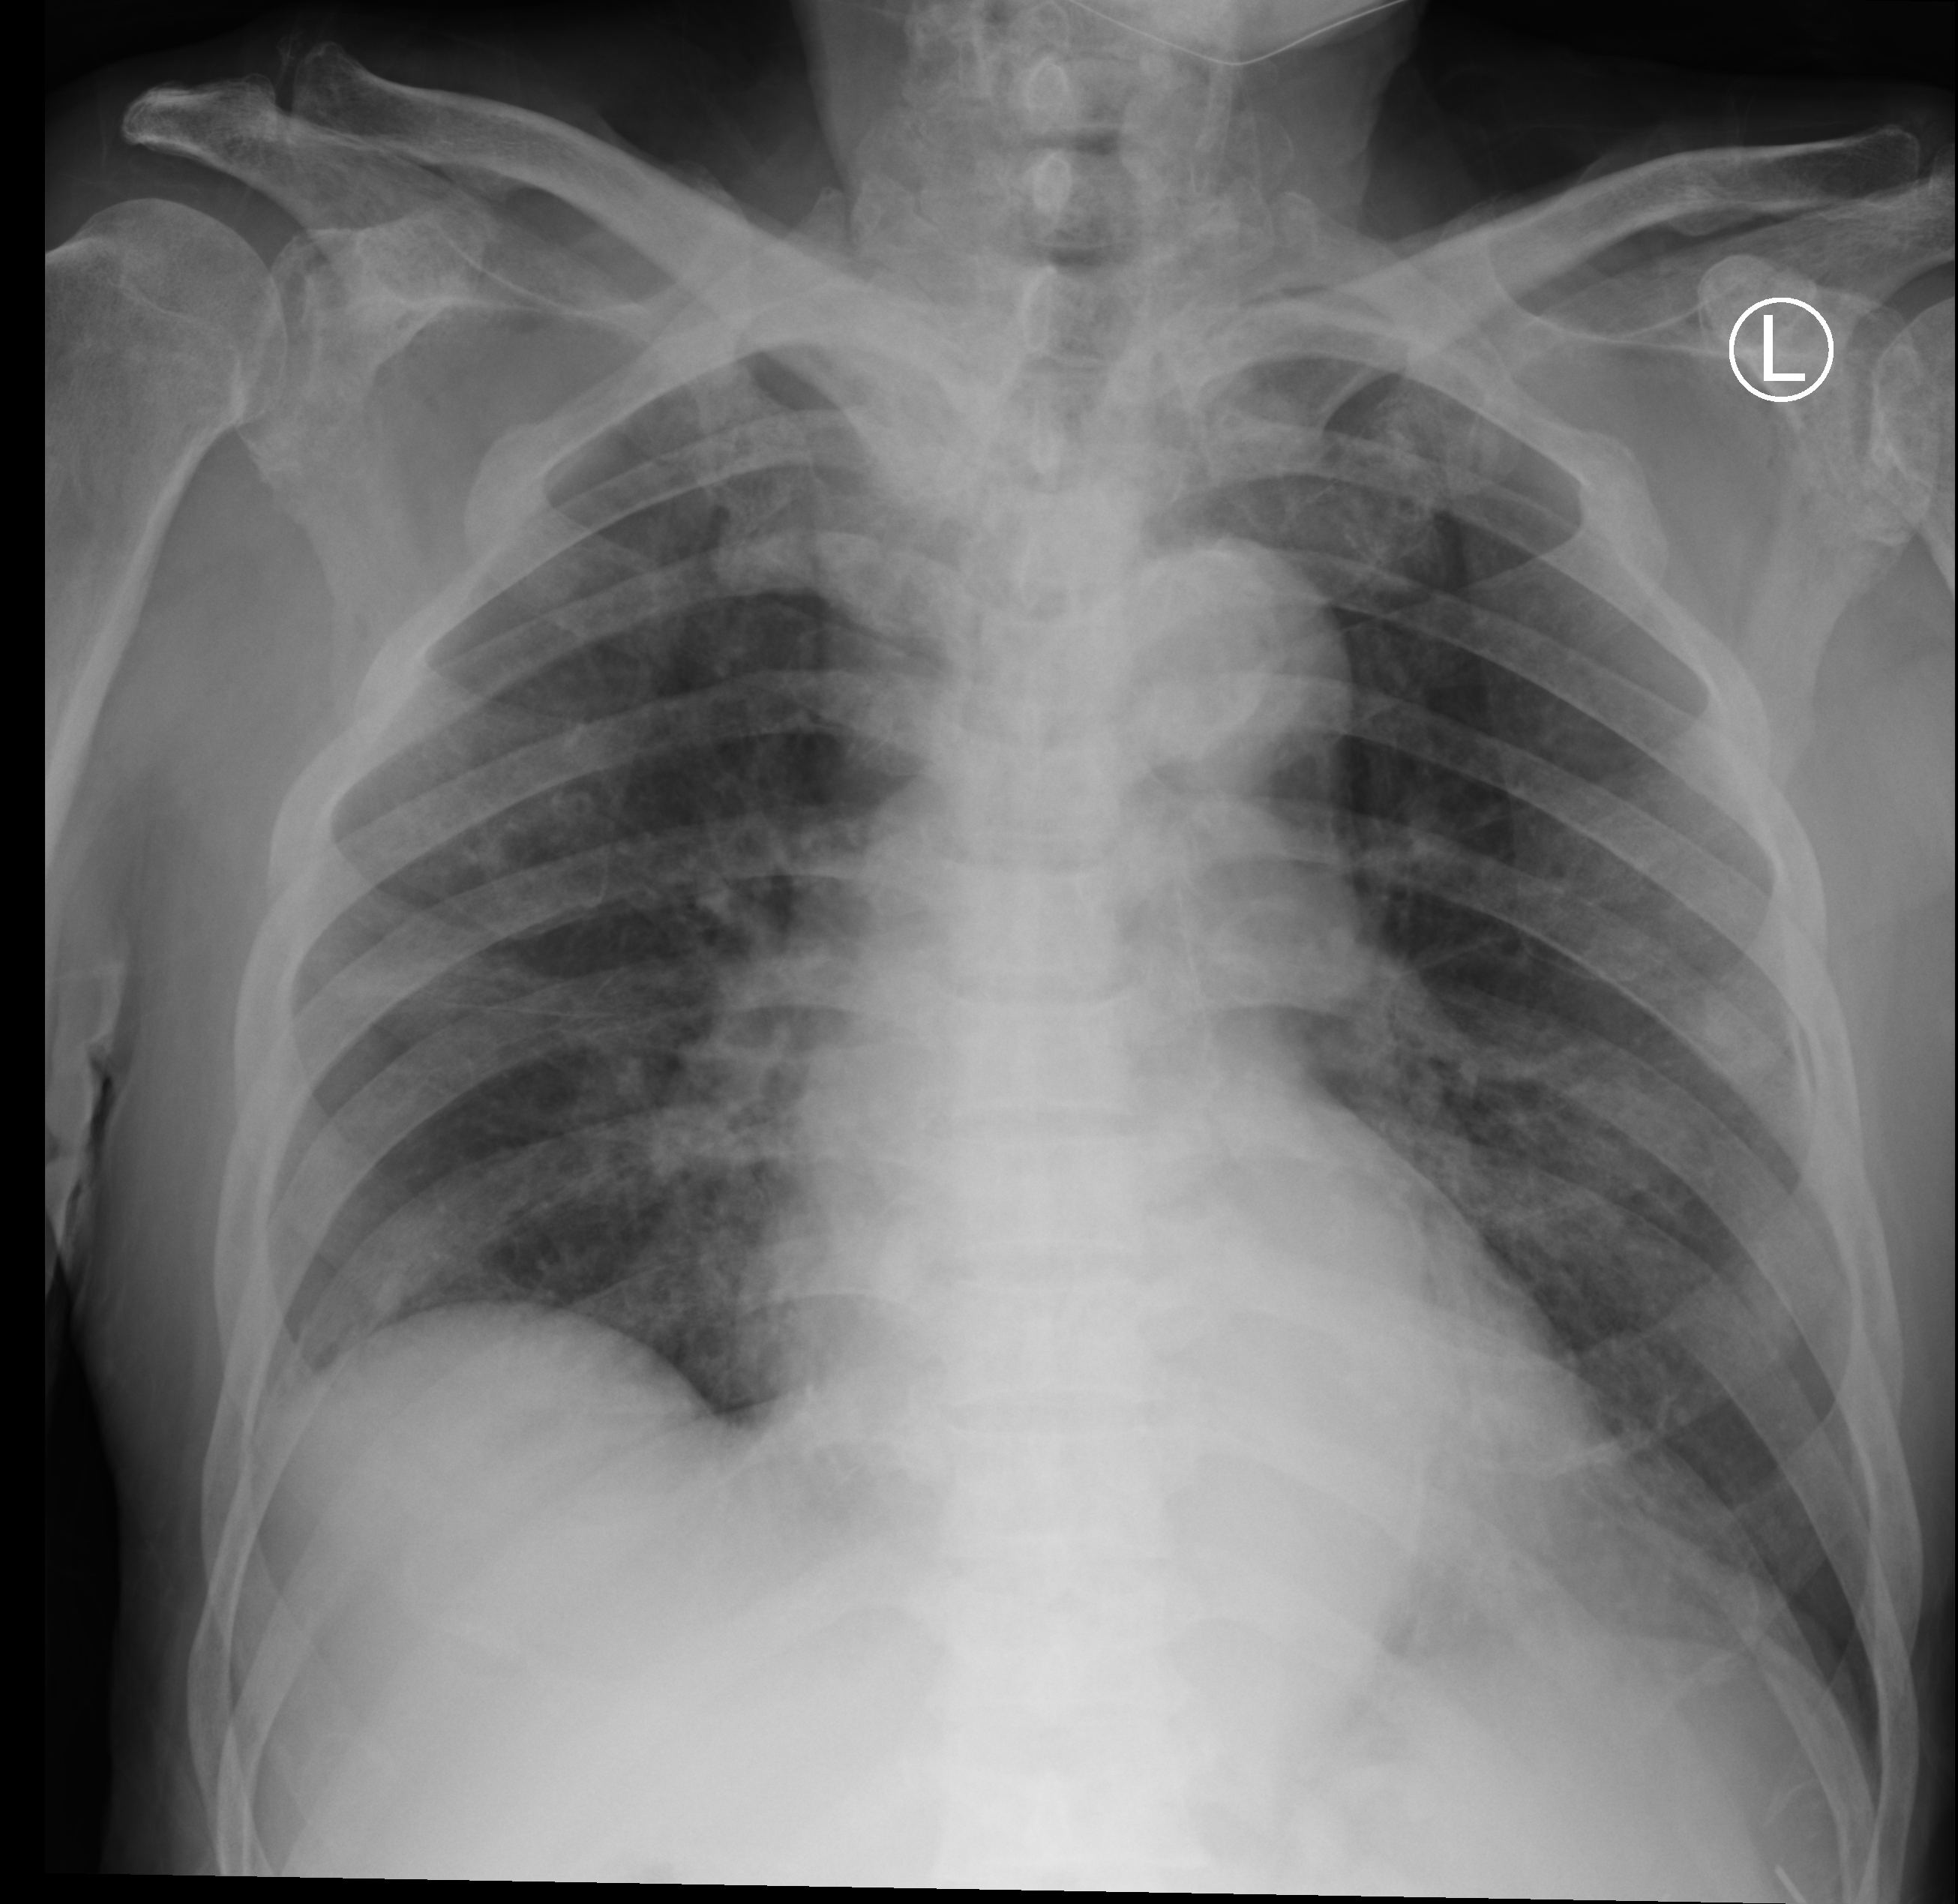
Bedside chest radiograph (computed radiography). Male patient hospitalised with COVID-19, age 75–90 years.
From the hospital-stay record, not from the radiograph (when in the stay this image was taken is not recorded): admitted to intensive care during this hospital stay: no.